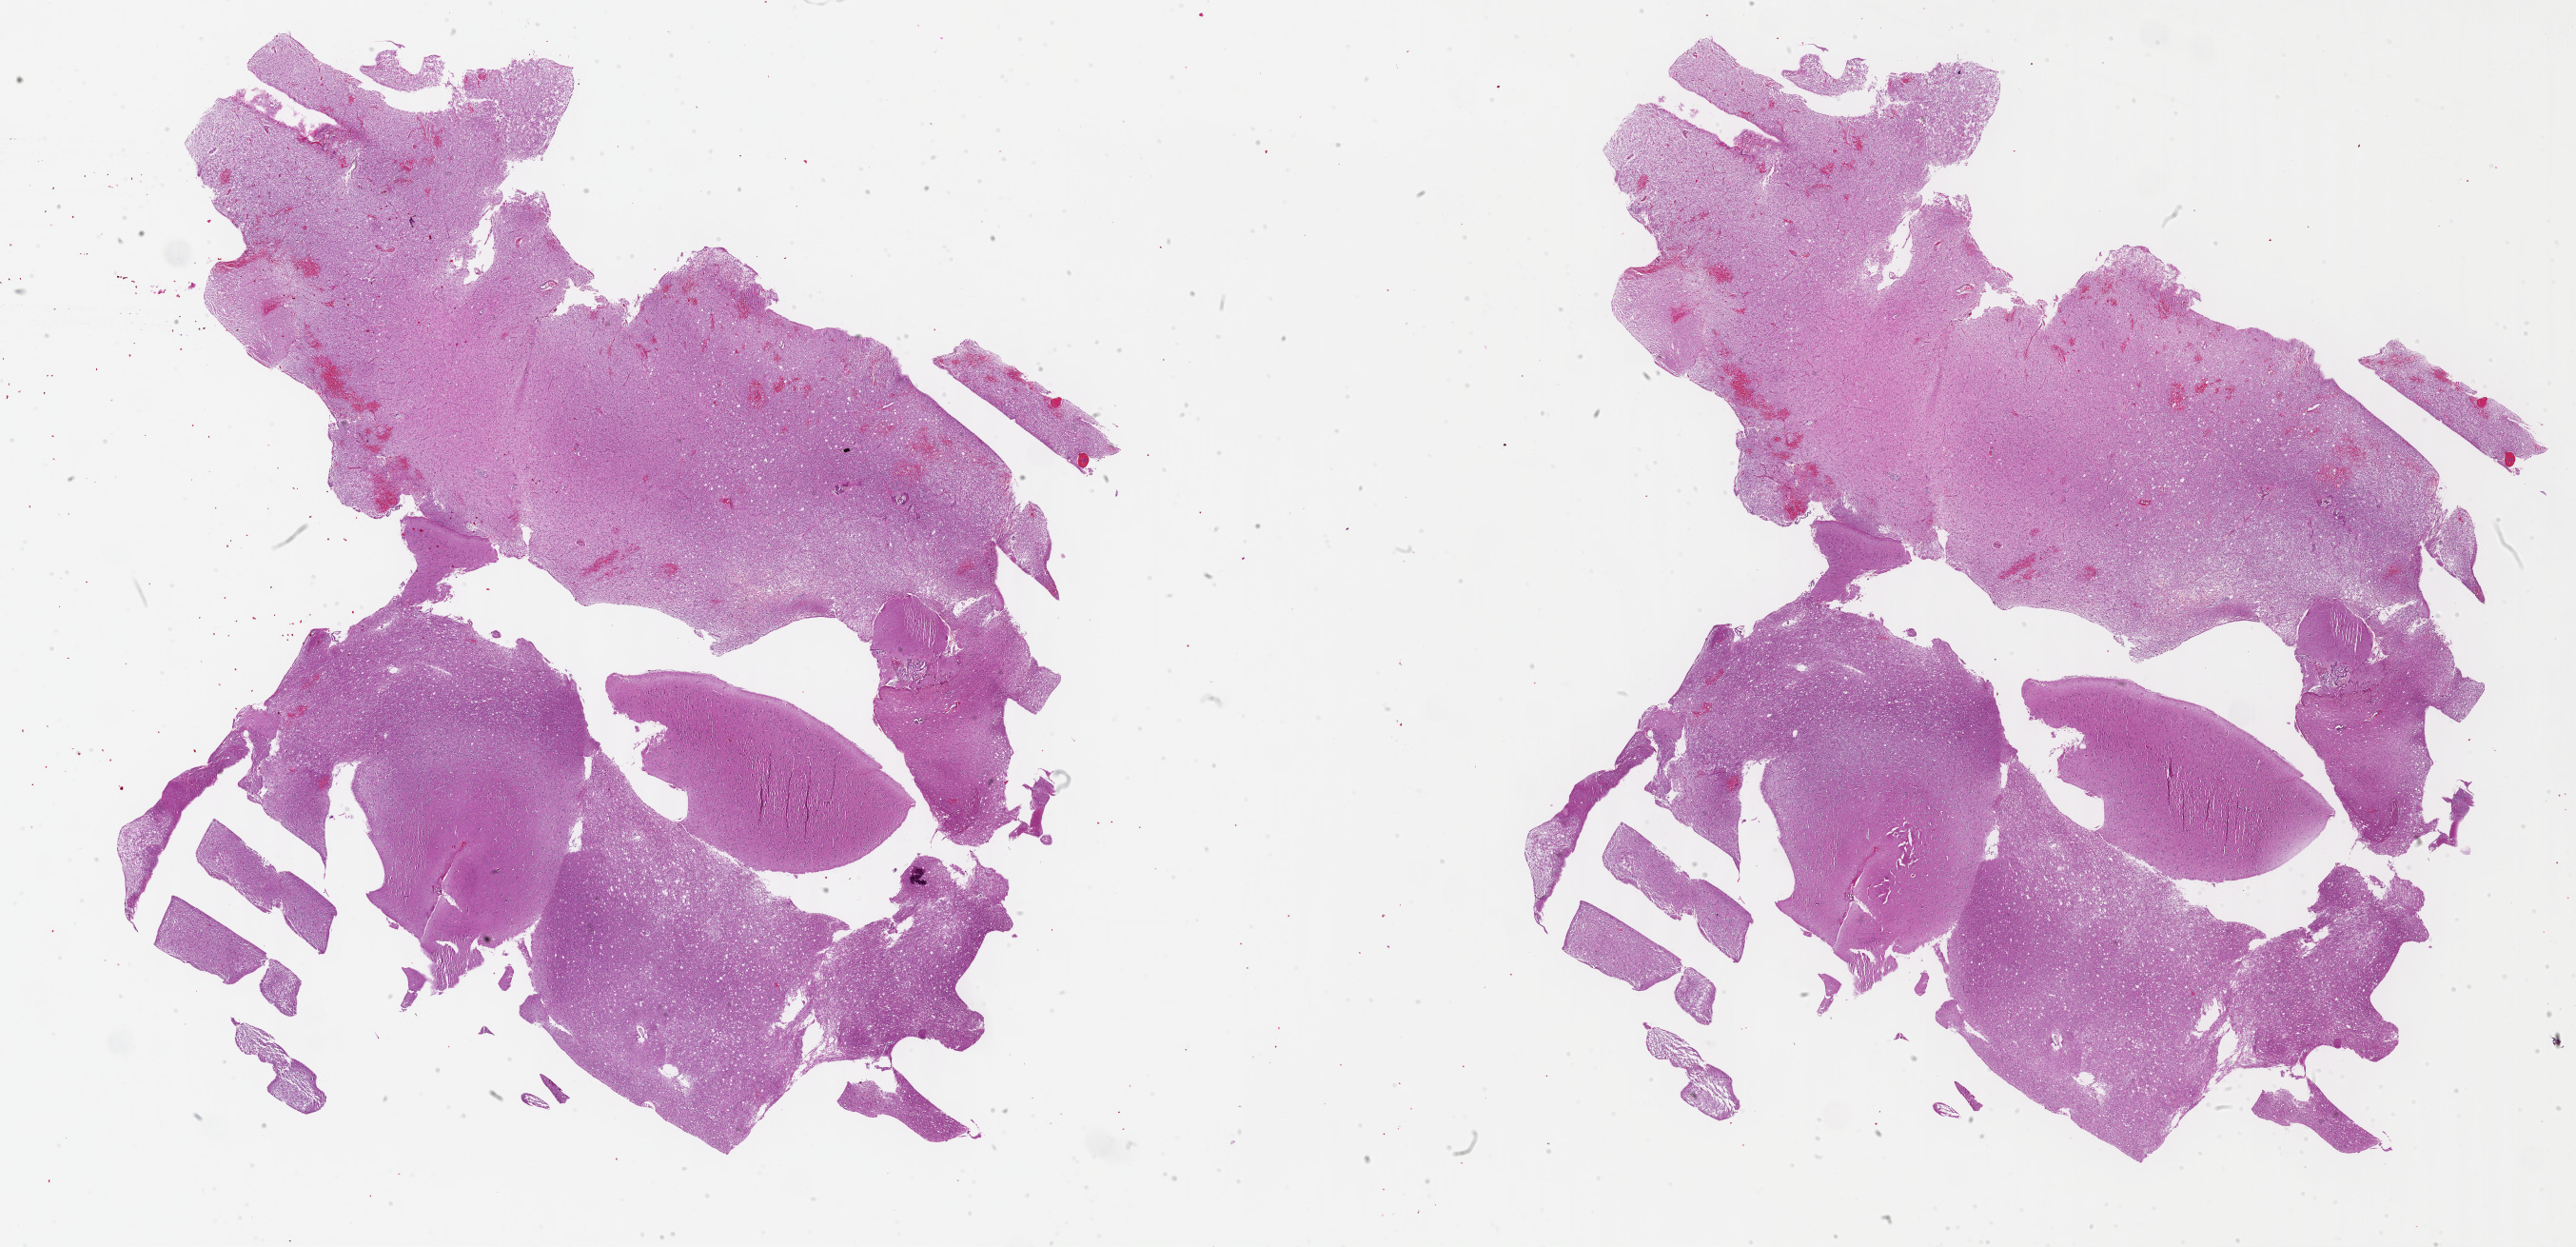
H&E whole-slide image — a low-resolution overview of the entire scanned area, about 43.8 x 21.2 mm, FFPE section, brain, primary tumour sample. Female, age 33 years at initial diagnosis. Histologic grade: G2 (moderately differentiated).
* pathologic diagnosis: Oligodendroglioma, NOS (cerebrum)